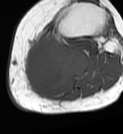
MRI of an extremity soft-tissue mass, one axial slice; position 40 of 68 along the scan axis; MR volume resampled by the dataset authors to the PET/CT grid (not the native acquisition matrix); 3.27 mm slice thickness; 123 × 134 image matrix, field of view 120 × 131 mm. Female patient. Case-level facts recorded for this patient, not image findings: histological type: extraskeletal high grade osteogenic sarcoma; grade: high; site of the primary tumour: left calf.
Structures marked on this image (expert contour drawn on MRI and transferred to this co-registered scan by the dataset authors):
- gross tumour volume (mass): bounding box [x1, y1, x2, y2] px = [24, 32, 89, 92]